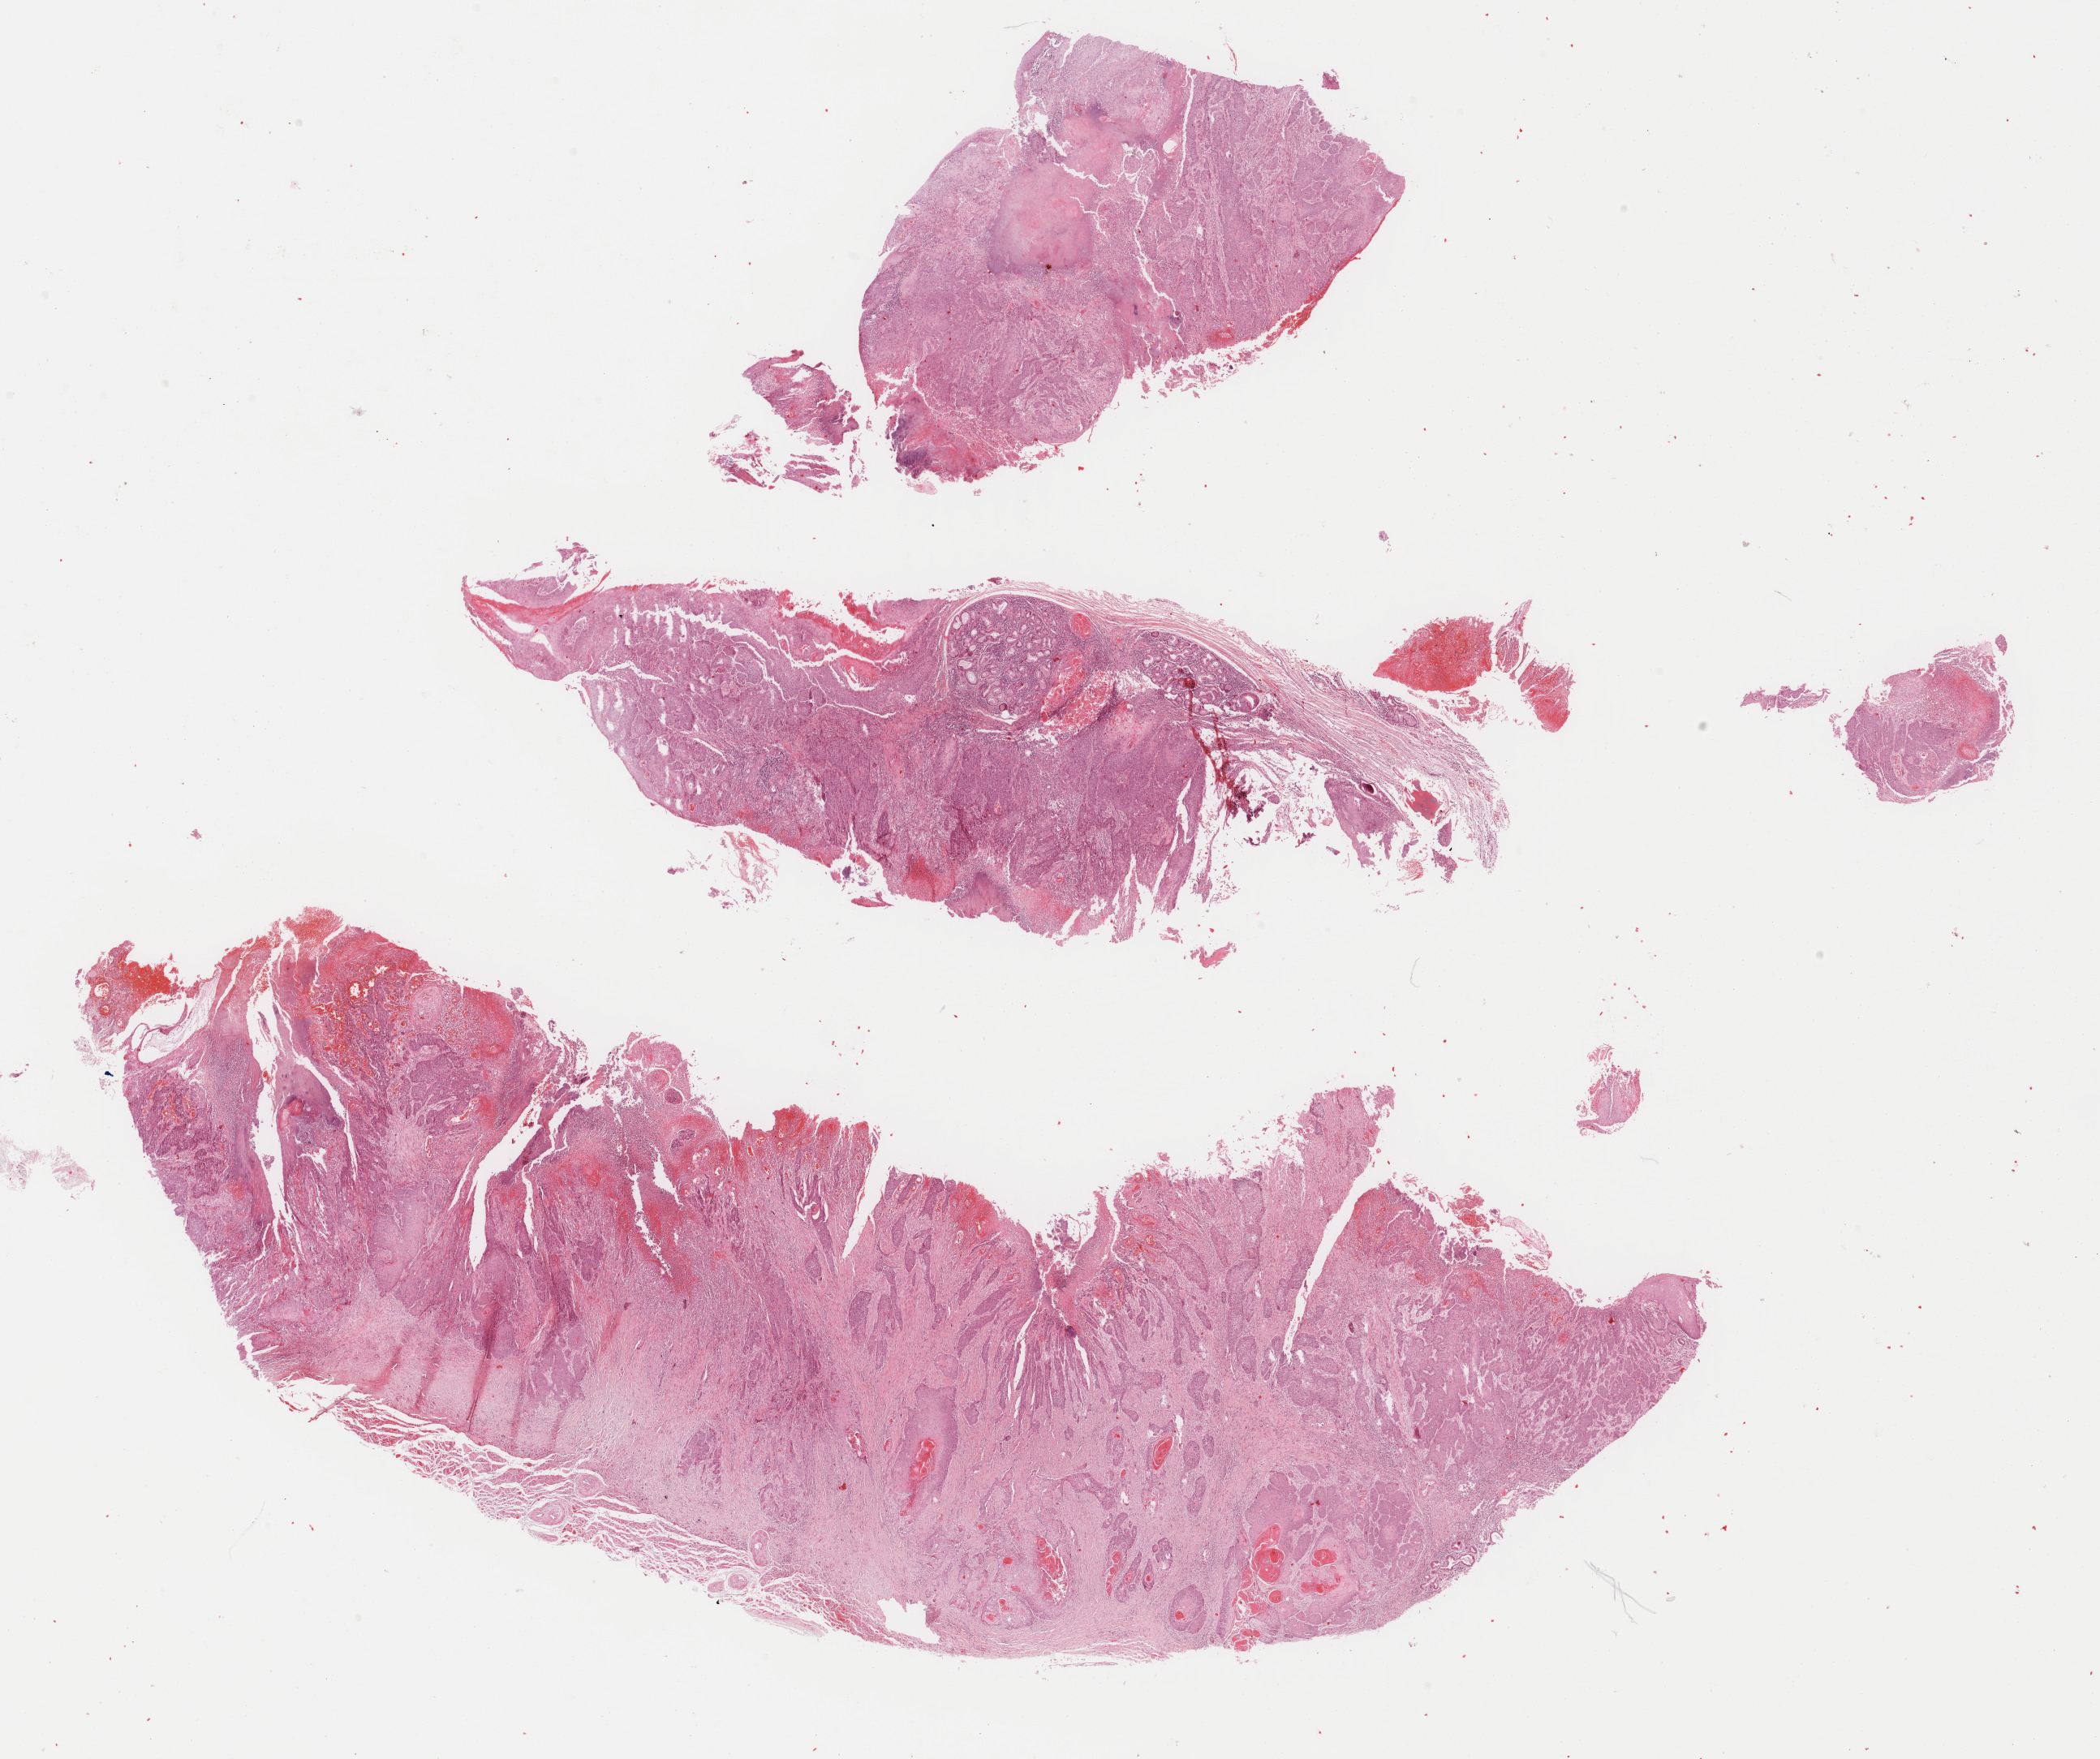
Digitized H&E-stained tissue section (whole slide), shown as a low-resolution overview of the whole scanned area (about 20.5 x 17.2 mm, slide scanned at 40x), formalin-fixed paraffin-embedded (FFPE) diagnostic section, sample: primary tumour, head and neck. Male, age 62 years at initial diagnosis. Histologic grade: G2 (moderately differentiated).
• laterality: left
• AJCC pathologic stage: II (7th edition)
• TNM: T2 N0 M0
• histologic diagnosis: Squamous cell carcinoma, keratinizing, NOS (larynx, NOS)
• lymph nodes positive (case pathology): 0 of 3 examined